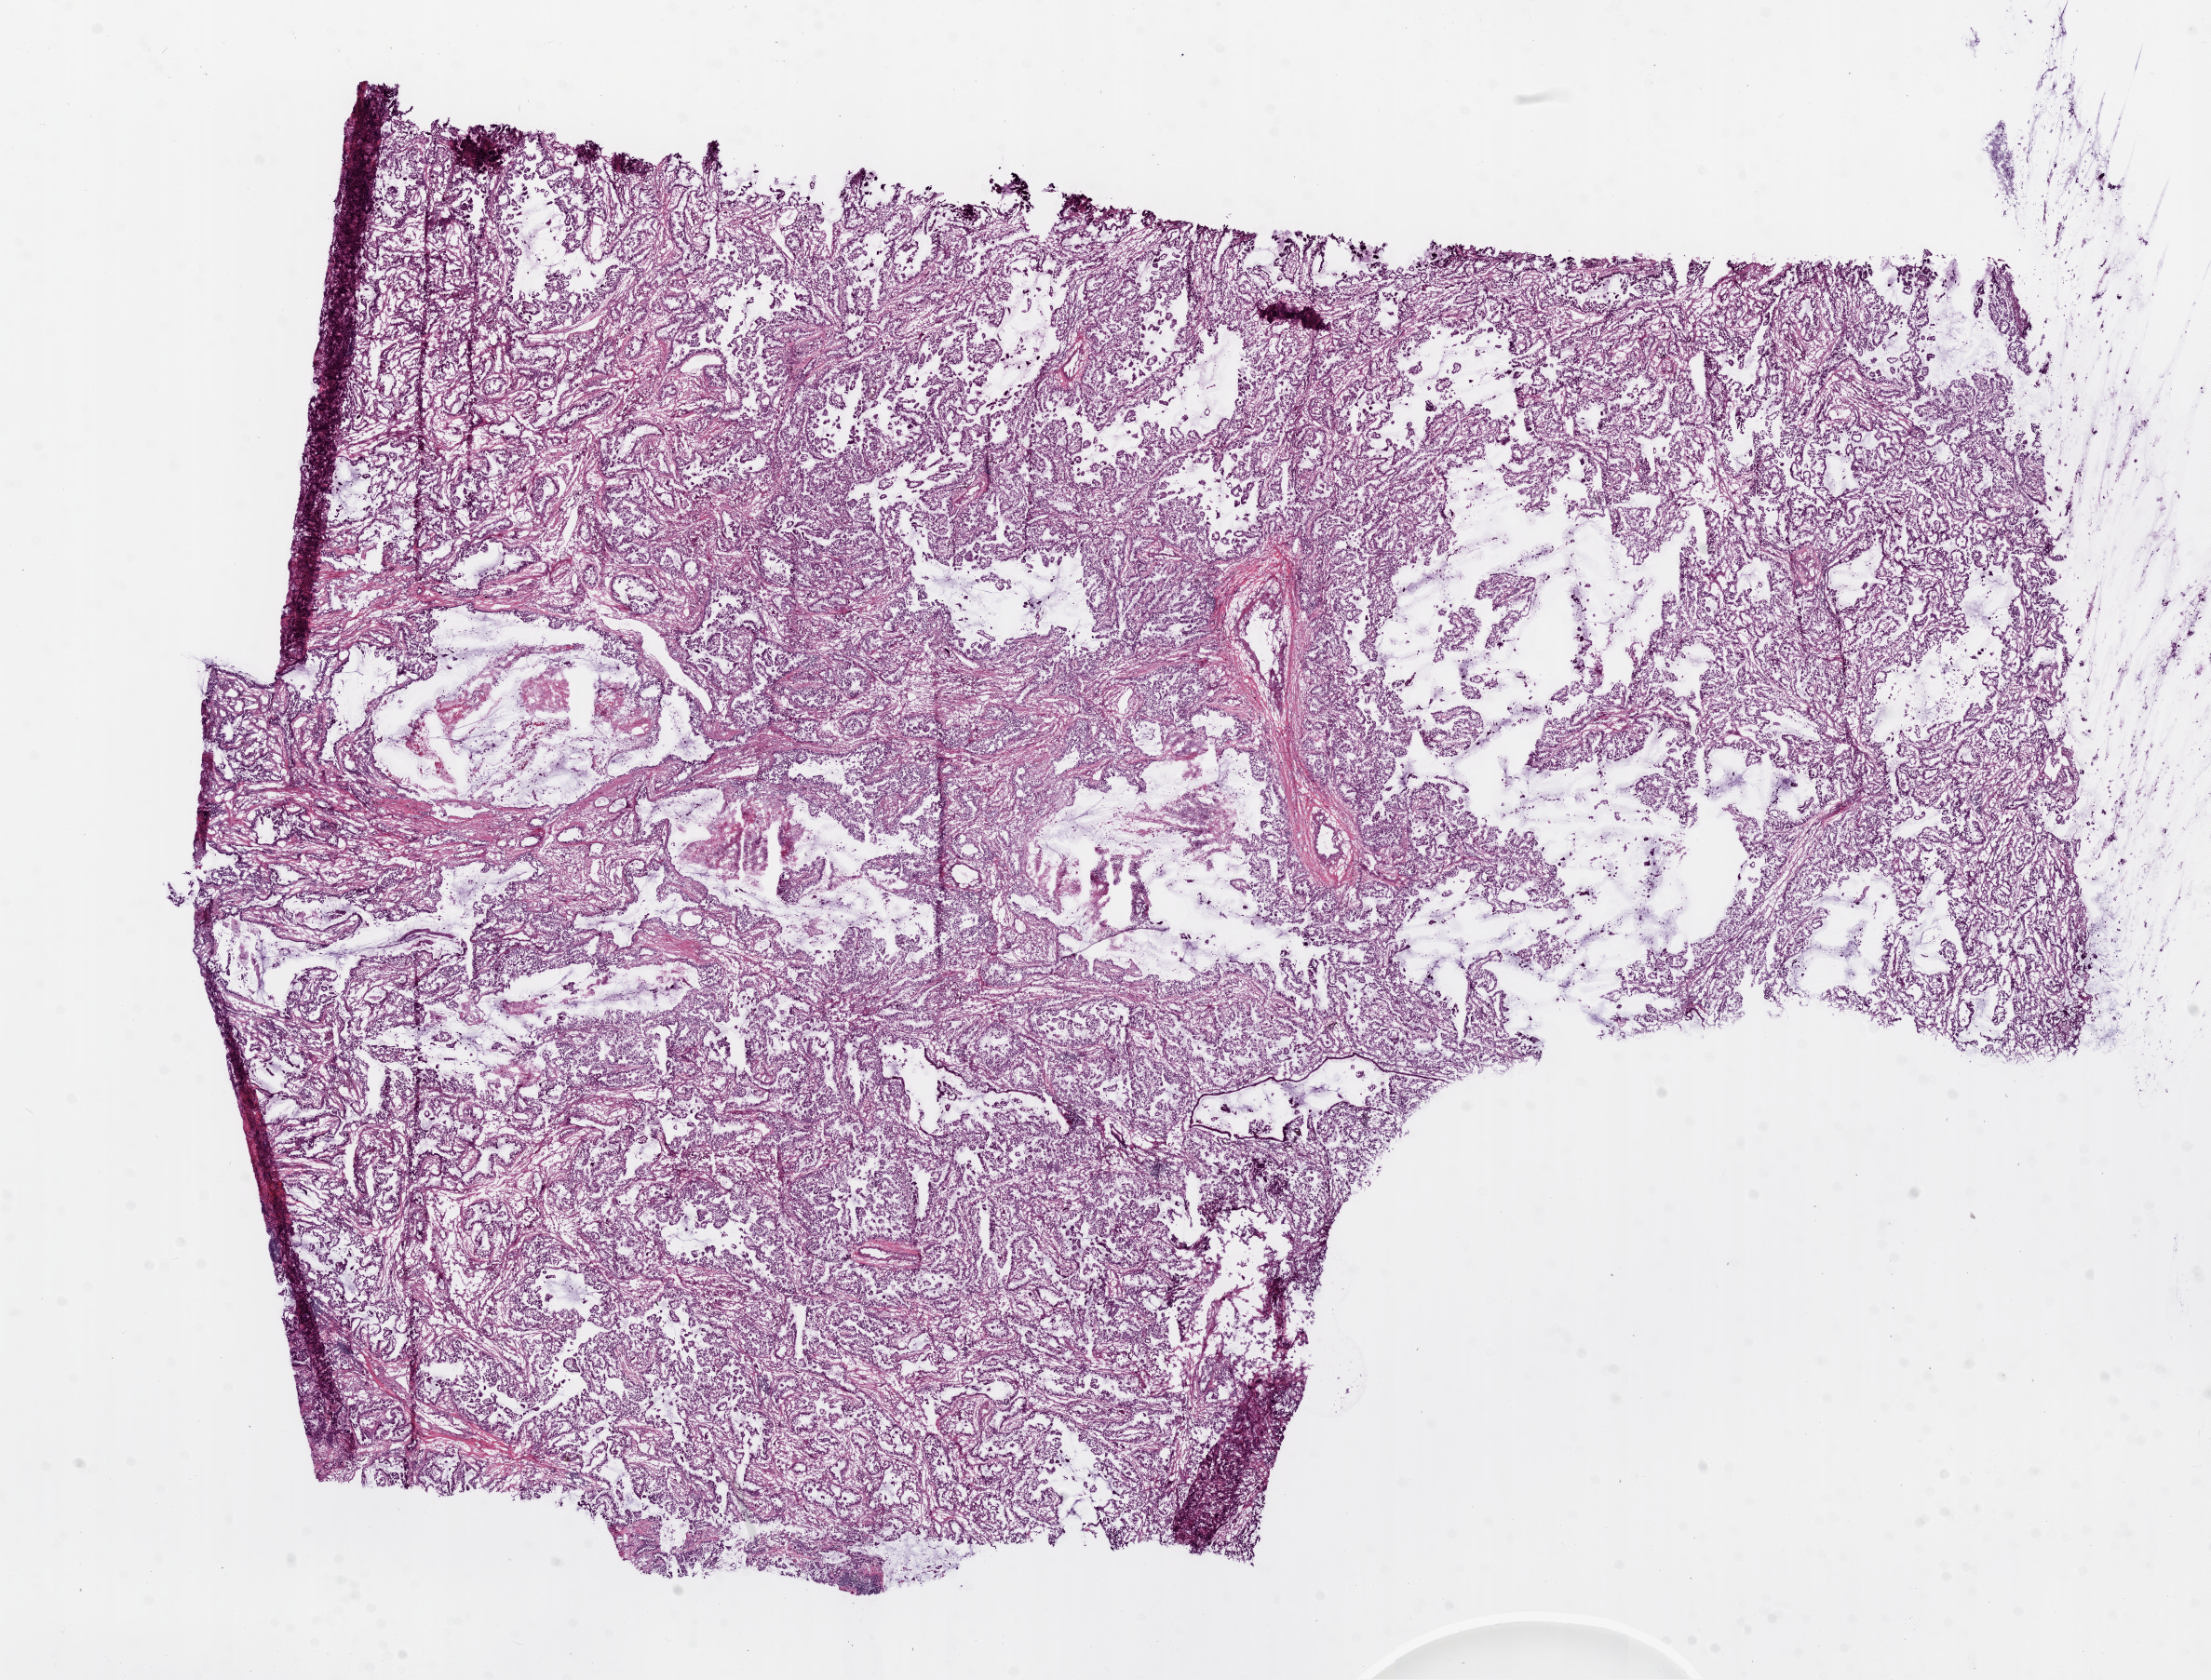
Whole-slide histology image, H&E — low-resolution overview of the scanned area, about 19.1 x 14.5 mm (from a 20x scan), frozen section from the bottom of the tissue portion, lung, primary tumour sample. Male patient; age at initial diagnosis 59 years. Composition of this section per pathologist review: tumour cells 50%, tumour nuclei 85%, normal cells 0%, stromal cells 50%, necrosis 0%.
Pathologic diagnosis: Adenocarcinoma, NOS (lower lobe, lung). AJCC pathologic stage: IIIA. Laterality: left.